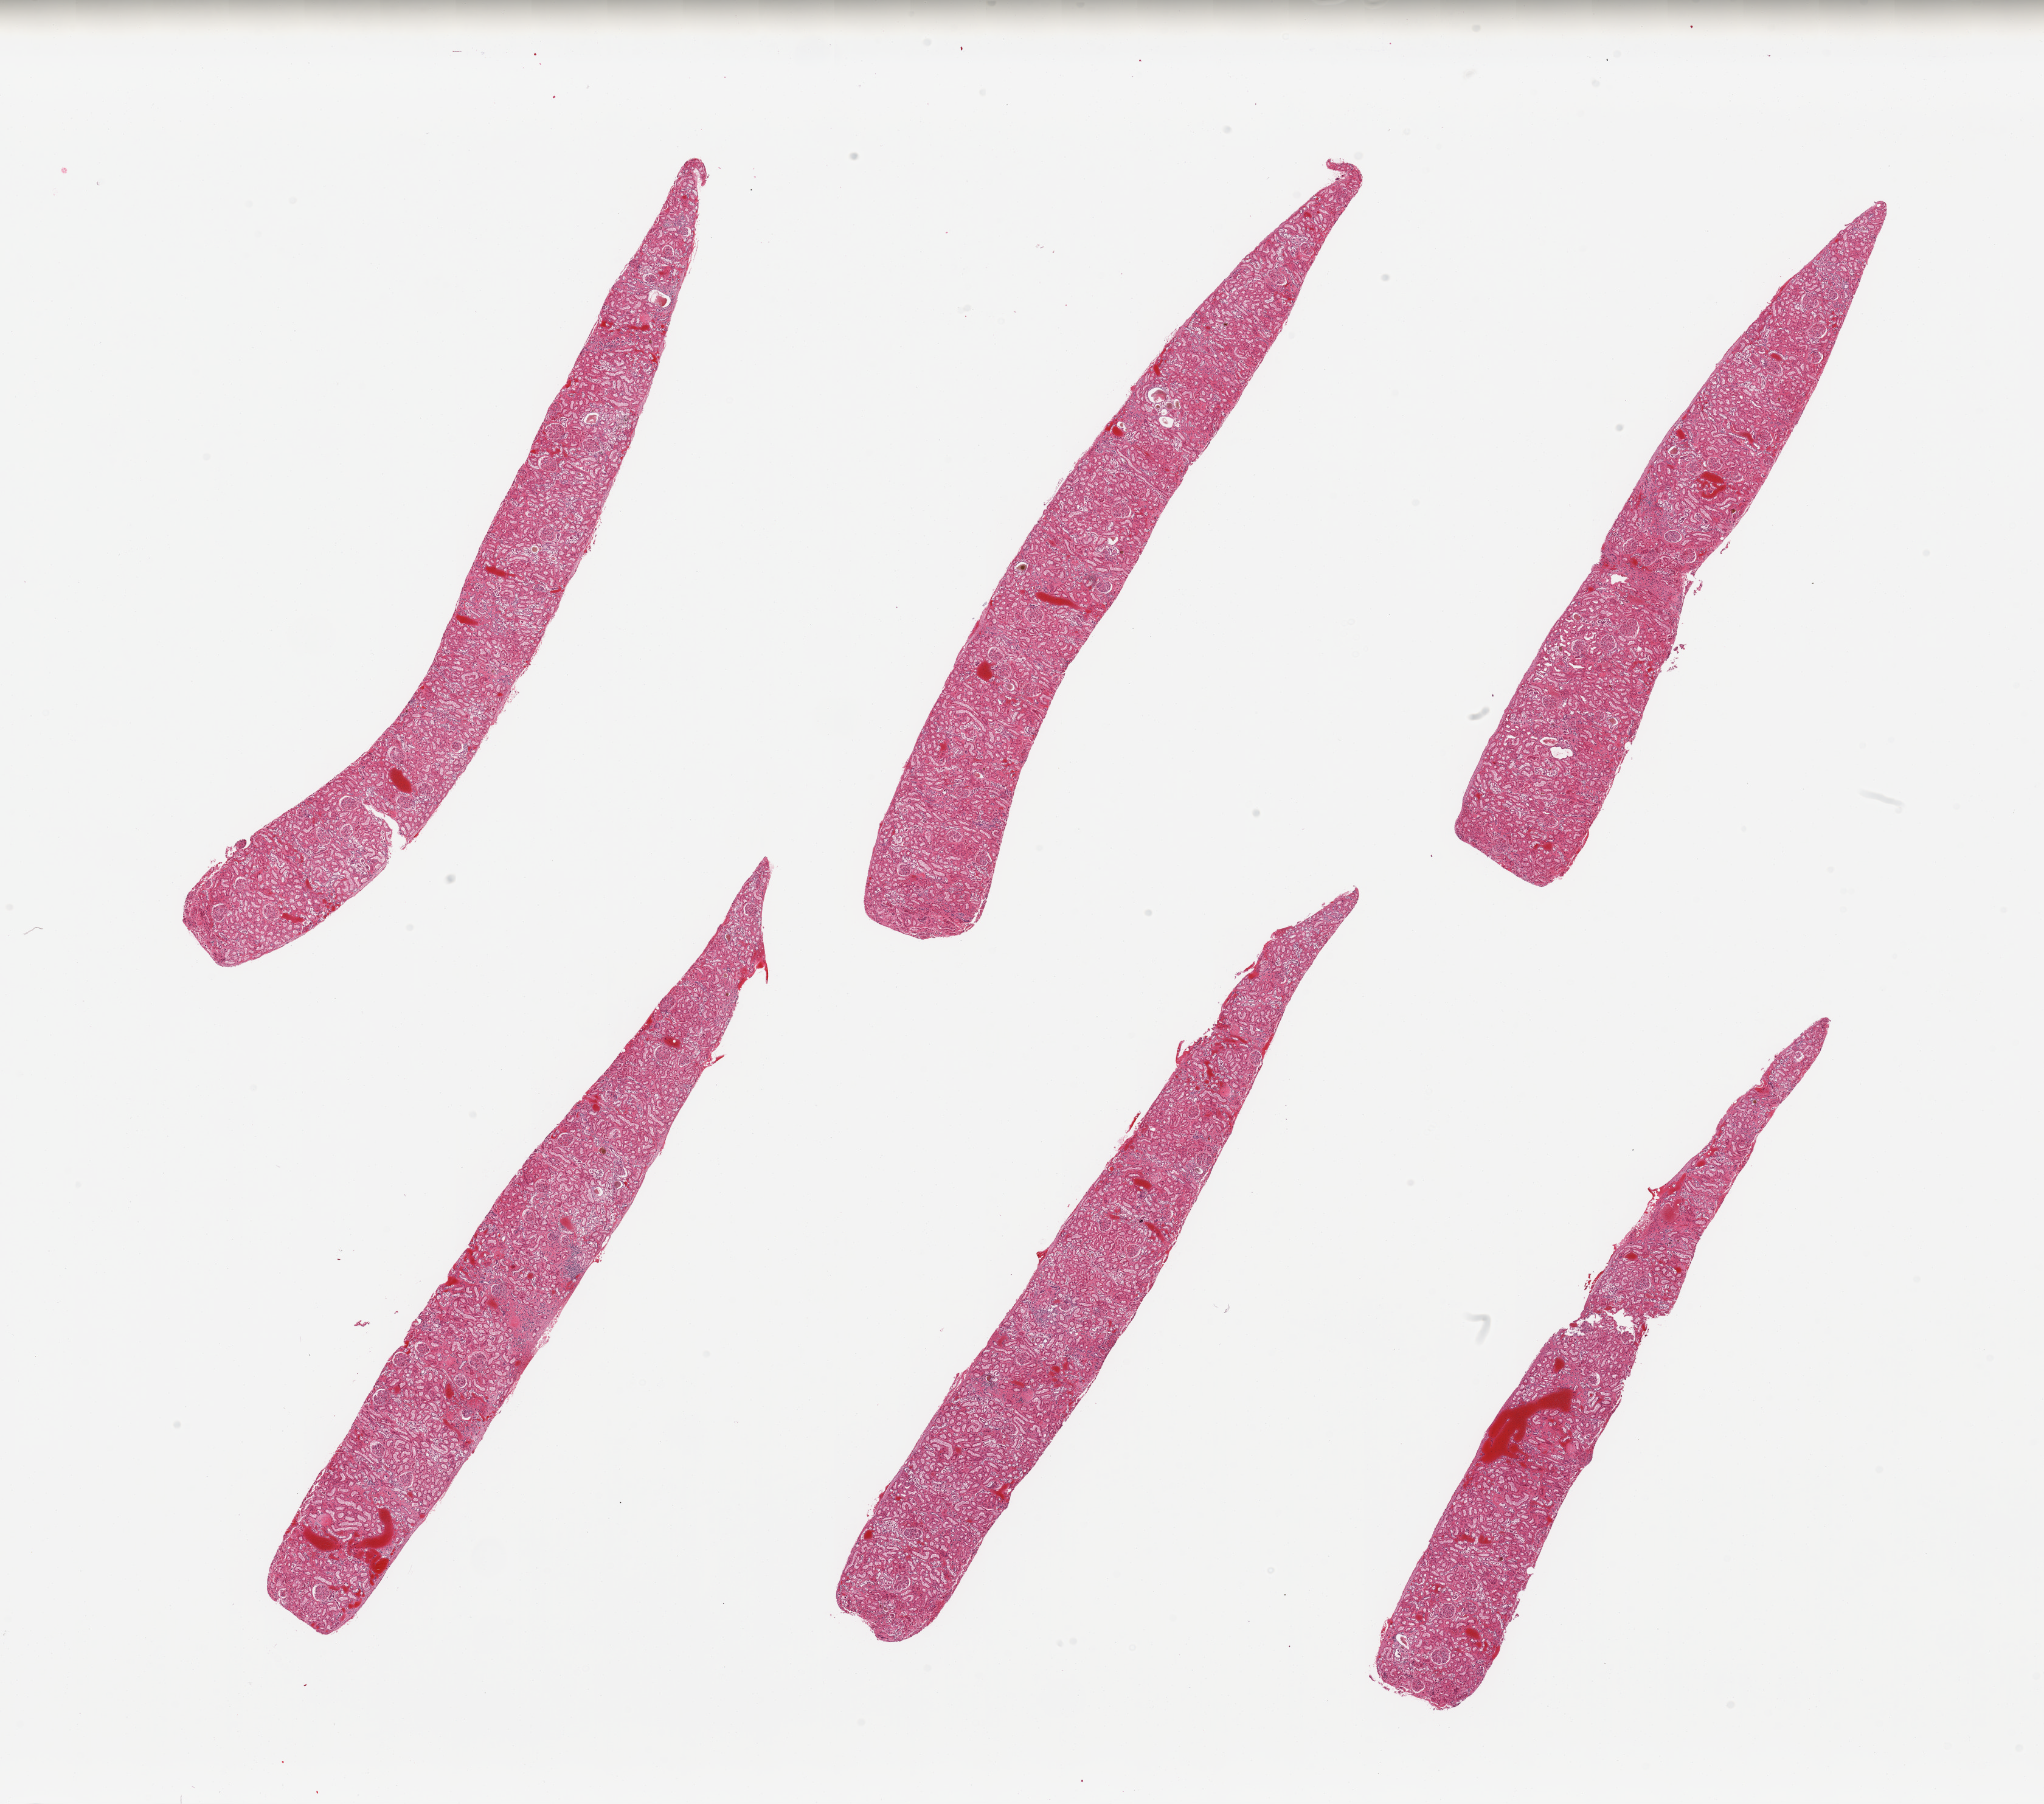
H&E whole-slide image — a low-resolution overview of the entire scanned area, about 26.6 x 23.5 mm. PAXgene-fixed paraffin-embedded (PFPE) section. Sampled site (target tissue): renal cortex. Tissue donor sample. Donor sex: male.
Reviewer comment on this tissue sample: 6 pieces; tubules variably autolyzed; no sign of active or chronic disease; focally congested.